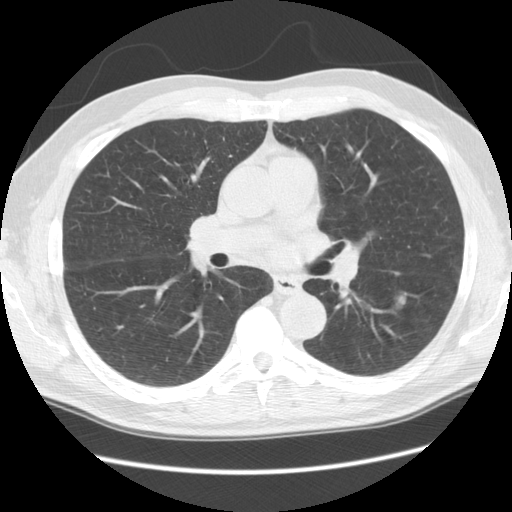
Axial slice from a low-dose chest CT screening exam; third annual screen; lung window (W 1500 / L -600 HU); 2.5 mm slice thickness; standard (soft-tissue) reconstruction kernel (STANDARD). Male participant, aged 60 years at enrolment. Current smoker at enrolment.
• Lesion marked by an expert reader, bounding box <381,288,418,319> (left, top, right, bottom; pixels).
• The screening reader recorded 5 non-calcified nodules or masses ≥4 mm on this exam; which of them this box marks is not recorded.
• Official screen result: positive, other.
• Participant outcome: lung cancer diagnosed 153 days after this screen — large cell neuroendocrine carcinoma, left lower lobe, poorly differentiated (G3), stage IB (AJCC 6th edition), 33 mm at pathology.